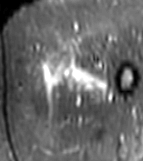
MRI of an extremity soft-tissue mass, one axial slice. Position 14 of 81 along the scan axis. STIR. MR volume resampled by the dataset authors to the PET/CT grid (not the native acquisition matrix). 3.27 mm slice thickness. 143 × 161 image matrix, field of view 140 × 157 mm. Female patient. Case-level facts recorded for this patient, not image findings: histological type: myxofibrosarcoma; grade: intermediate; site of the primary tumour: left thigh.
Structures marked on this image (expert contour drawn on MRI and transferred to this co-registered scan by the dataset authors):
- gross tumour volume including surrounding oedema: bounding box (x1, y1, x2, y2) in pixels: (37, 58, 112, 100)
- gross tumour volume (mass): (72, 58, 96, 68)